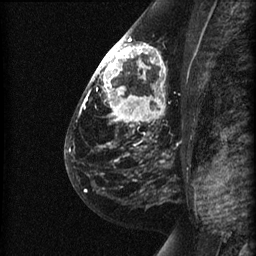
Breast MRI (dynamic contrast-enhanced), one sagittal slice. Slice 36 of 60 in the series (ordered by position). Dynamic contrast-enhanced series, image 2 of 3 at this slice position (ordered by acquisition). 1.5 T. TE 4.2 ms, TR 22.7 ms. 1.5 mm slice thickness. 256 × 256 image matrix, field of view 180 × 180 mm. Female patient, age 48 years. From the clinical record (not read from this slice): setting: breast cancer imaged before/during neoadjuvant chemotherapy; receptor status: triple-negative.
Annotated regions visible in this slice (semi-automatic segmentation, software-assisted and operator-edited):
- analysis volume of interest (the breast-tissue region the enhancement analysis was run in; not a lesion): bounding box (x1, y1, x2, y2) in pixels: (89, 27, 191, 180)
- tumour enhancement mask (voxels above the 90 % enhancement threshold inside the analysis volume of interest): (92, 35, 163, 109)